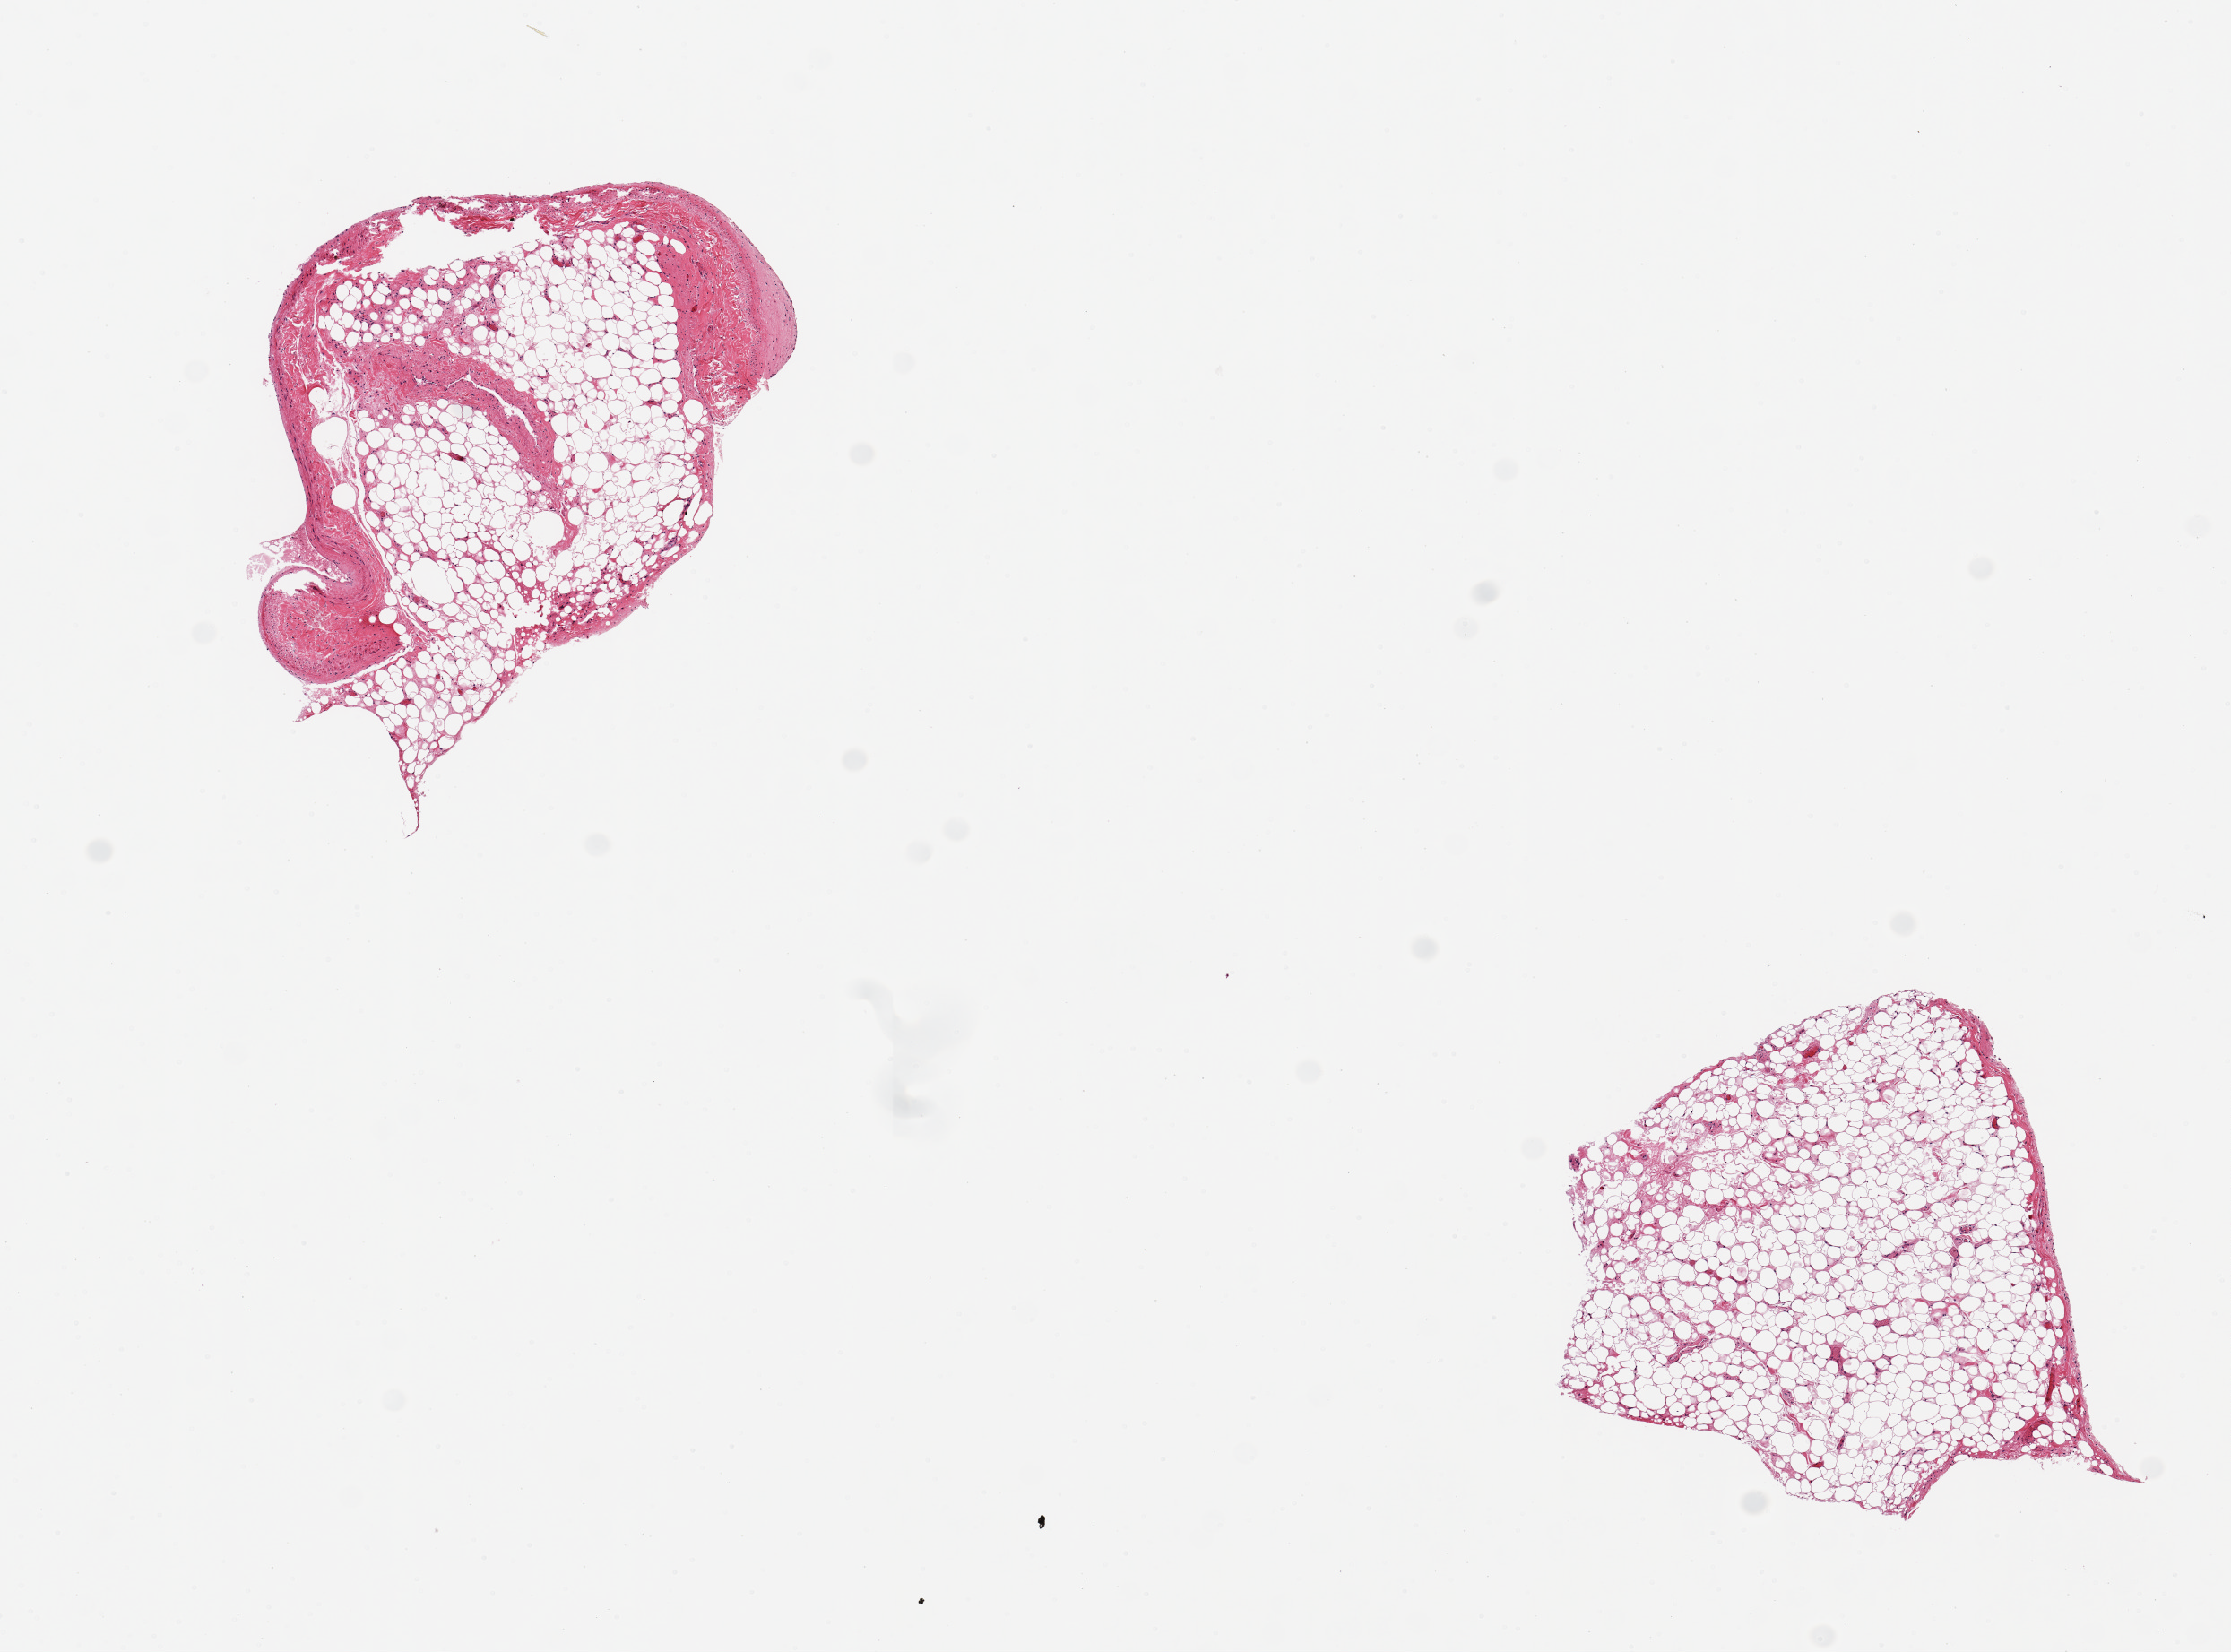
Hematoxylin and eosin (H&E) whole-slide image — low-resolution overview of the scanned area, about 9.8 x 7.3 mm (acquisition: 20x scan); PAXgene-fixed paraffin-embedded (PFPE) section; section of coronary artery (target tissue); donor tissue sample. Male donor.
• review note (as recorded): 2 pieces 2x2 mm; 1 ~80% adipose; other 100% adipose